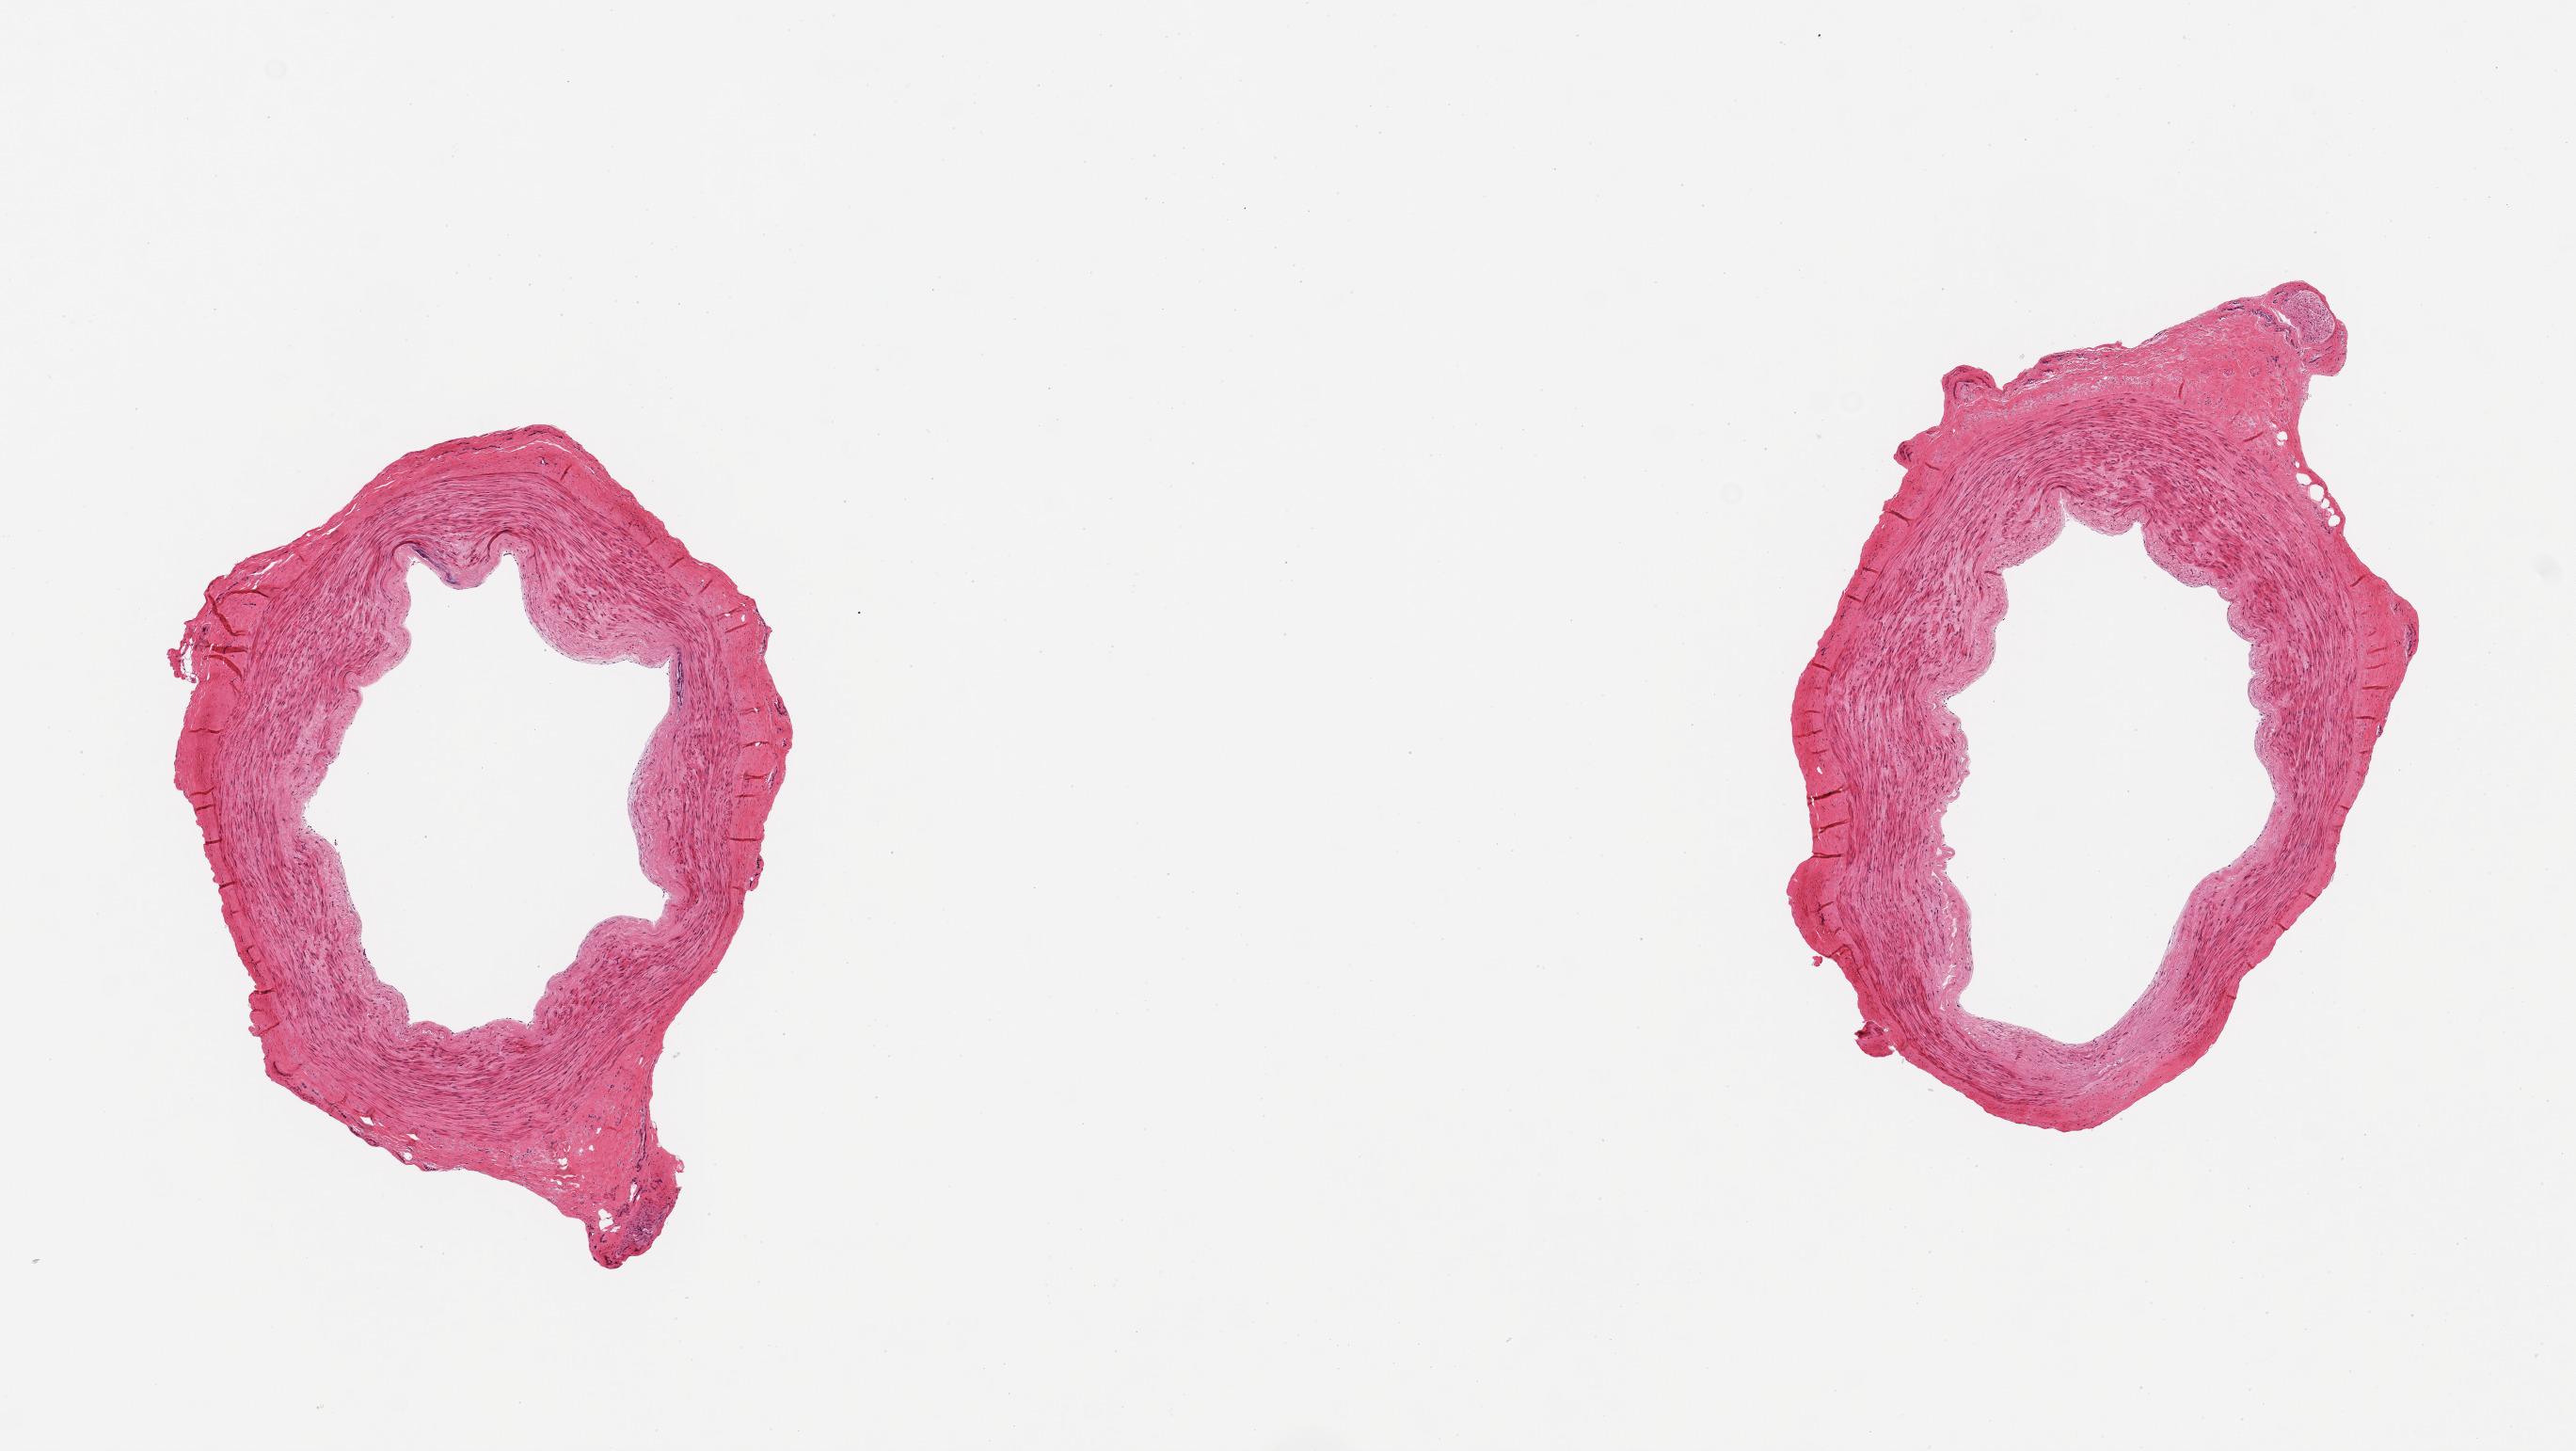
Digitized hematoxylin and eosin (H&E)-stained section — a low-resolution overview of the entire scanned area, about 10.8 x 6.1 mm, PAXgene-fixed, paraffin-embedded tissue, section of tibial artery (target tissue), donor tissue sample.
Reviewer comment on this tissue sample: 2 pieces, no adherent fat or significant atherosis.